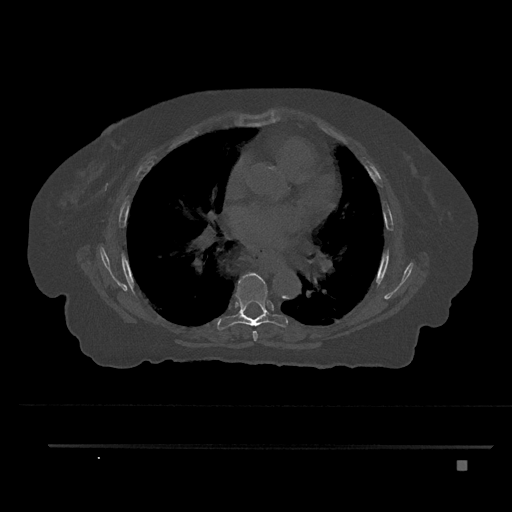
CT including the spine, one axial slice; position 493 of 797 along the scan axis; bone window (W 1800 / L 400 HU); 512 × 512 image matrix. Female patient, age 76 years. Case-level facts recorded for this patient, not image findings: primary cancer: lung; vertebrae with lytic lesions (as recorded): T11, L3.
Outlined on this slice (semi-automatically segmented with operator editing):
- T6 vertebra: bounding box (x1, y1, x2, y2) in pixels: (252, 330, 258, 341)
- T7 vertebra: (217, 273, 288, 331)